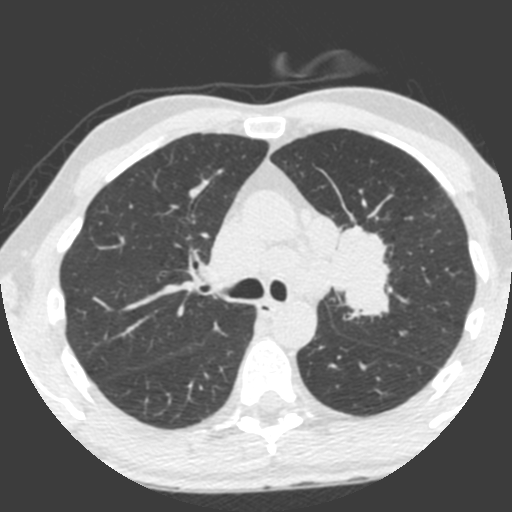
Chest CT (low-dose screening protocol), one axial image. Third screening round (two years after baseline). Lung window (W 1500 / L -600 HU). Male participant, aged 55 years at enrolment. Current smoker at enrolment.
Expert-annotated lung lesion, bounding box (x1, y1, x2, y2) in pixels: (309, 225, 394, 323). The exam's reader record, not a measurement of the box and not confirmed to be the same lesion: non-calcified nodule or mass ≥4 mm, left upper lobe, 49 × 29 mm, spiculated (stellate) margins, soft tissue attenuation, pre-existing on the prior screen: yes; interval growth: yes.